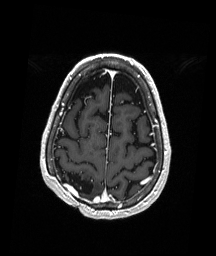
Brain MRI from a brain-tumour surgery series, one axial slice. Position 54 of 192 along the scan axis. T1-weighted post-contrast. 1 mm slice thickness. 216 × 256 image matrix, field of view 211 × 250 mm. From the clinical record (not read from this slice): histopathology: Astrocytoma; WHO grade: 3; IDH mutation: yes; tumour location: Right Parietal.
Annotated regions visible in this slice (expert manual segmentation):
- previous resection cavity: bounding box <62,172,94,195> (left, top, right, bottom; pixels)